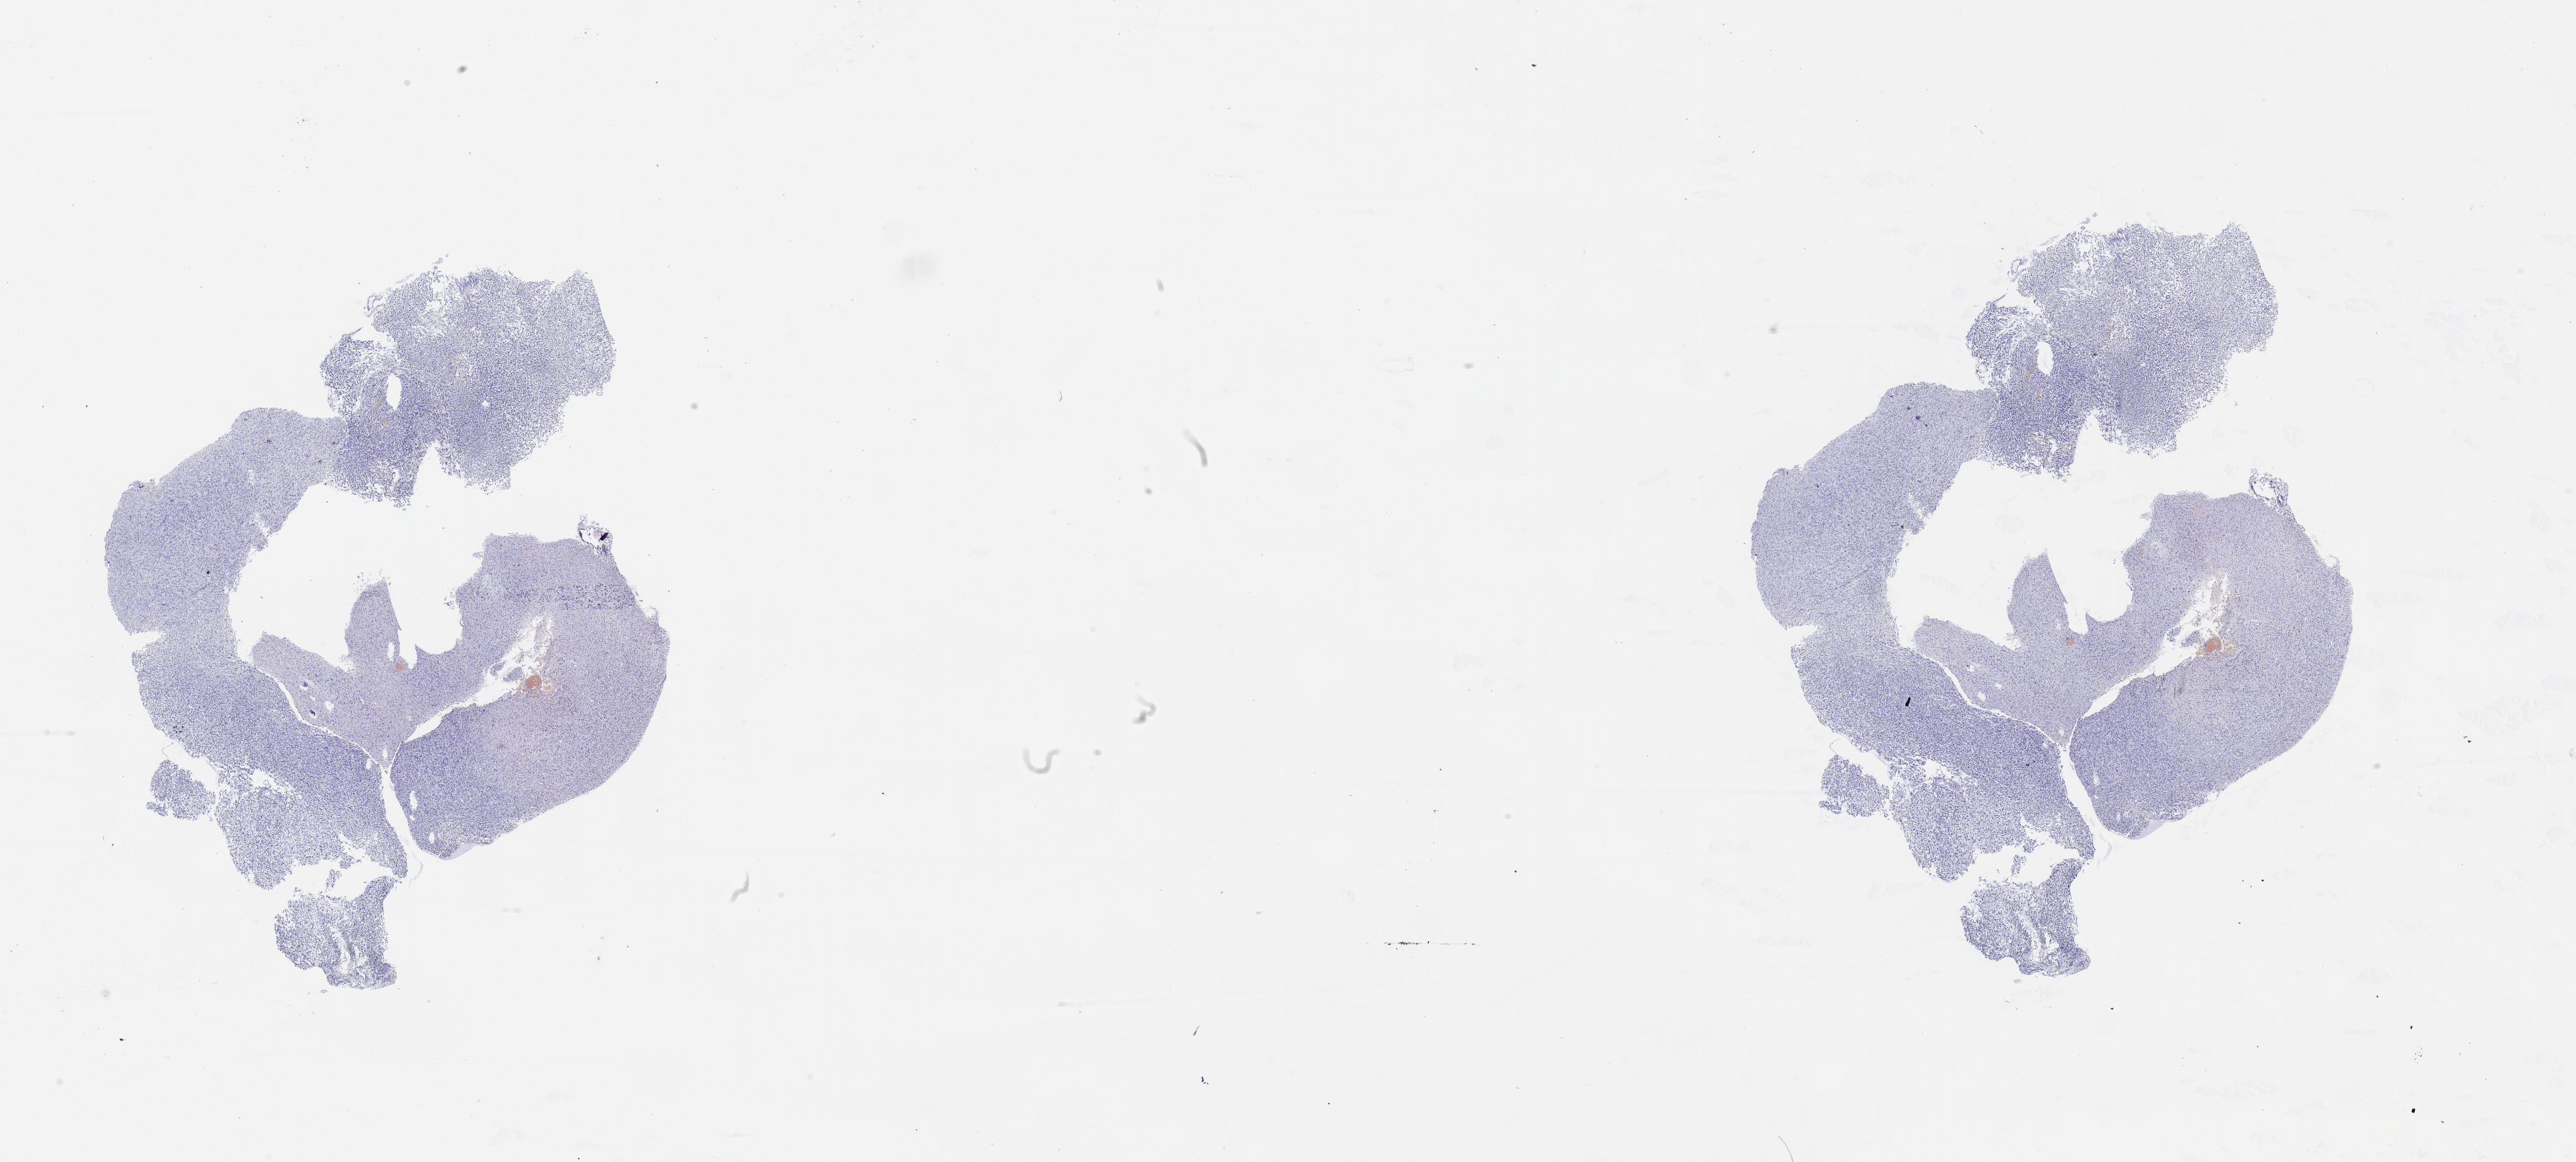
Digitized Hematoxylin and eosin (H&E) stained tissue section (whole slide) — a low-resolution overview of the entire scanned area, about 31.1 x 14.0 mm (acquisition: 20x scan), brain, tumour tissue. 36-year-old male patient.
• histologic diagnosis: Glioblastoma
• primary tumour site (as recorded): frontal lobe